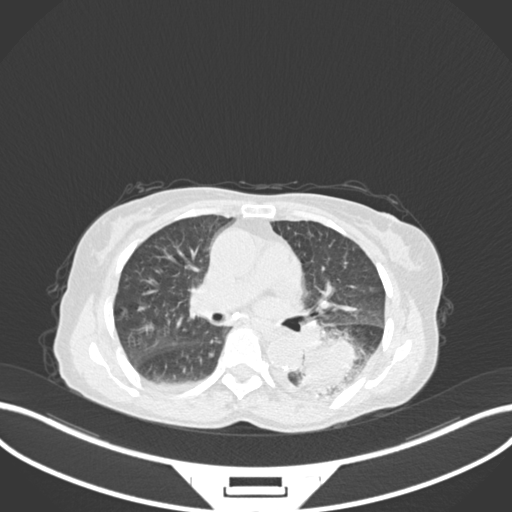
Chest CT, one axial slice; position 97 of 233 along the scan axis; lung window (W 1500 / L -600 HU); 1 mm slice thickness; 512 × 512 image matrix, field of view 400 × 400 mm. Patient: female, 78 years. Case-level facts recorded for this patient, not image findings: clinical TNM (as recorded): T3 N0 M1.
Structures marked on this image (rectangle marked by the reading radiologist):
- lung tumour (recorded histology: squamous cell carcinoma): bounding box <294,333,365,399> (left, top, right, bottom; pixels)